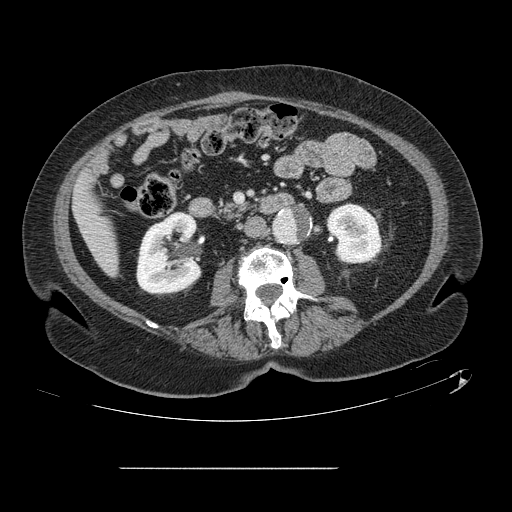
Contrast-enhanced abdominal CT, one axial slice; position 28 of 148 along the scan axis; 120 kVp; intravenous contrast given; soft-tissue window (W 400 / L 40 HU); 2.5 mm slice thickness; 512 × 512 image matrix, field of view 439 × 439 mm. Female patient, age 75 years. From the clinical record (not read from this slice): diagnosis: colorectal cancer liver metastases, imaged before liver resection.
Structures marked on this image (manually delineated by an expert):
- liver: bounding box <76,177,117,274> (left, top, right, bottom; pixels)
- planned liver remnant (the part of the liver to remain after resection): <76,177,117,273>